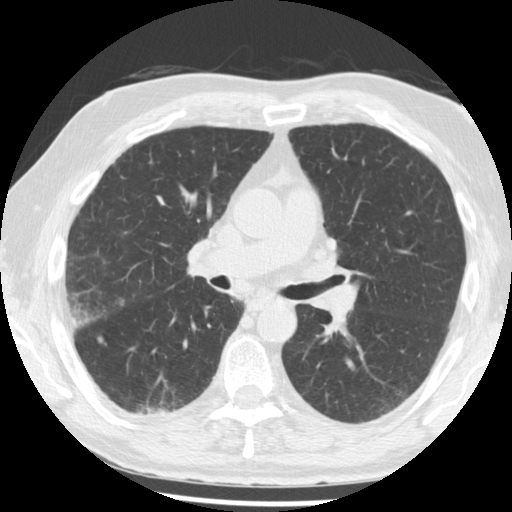
Low-dose screening chest CT, one axial slice; slice 118 of 221 in the series (ordered by position); reconstruction kernel STANDARD; 120 kVp; lung window (W 1500 / L -600 HU); 512 × 512 image matrix, field of view 350 × 350 mm.
Annotated regions visible in this slice (manually delineated by an expert):
- lesion 1 (tumor, lower lobe of right lung): bounding box <139,408,175,416> (left, top, right, bottom; pixels)